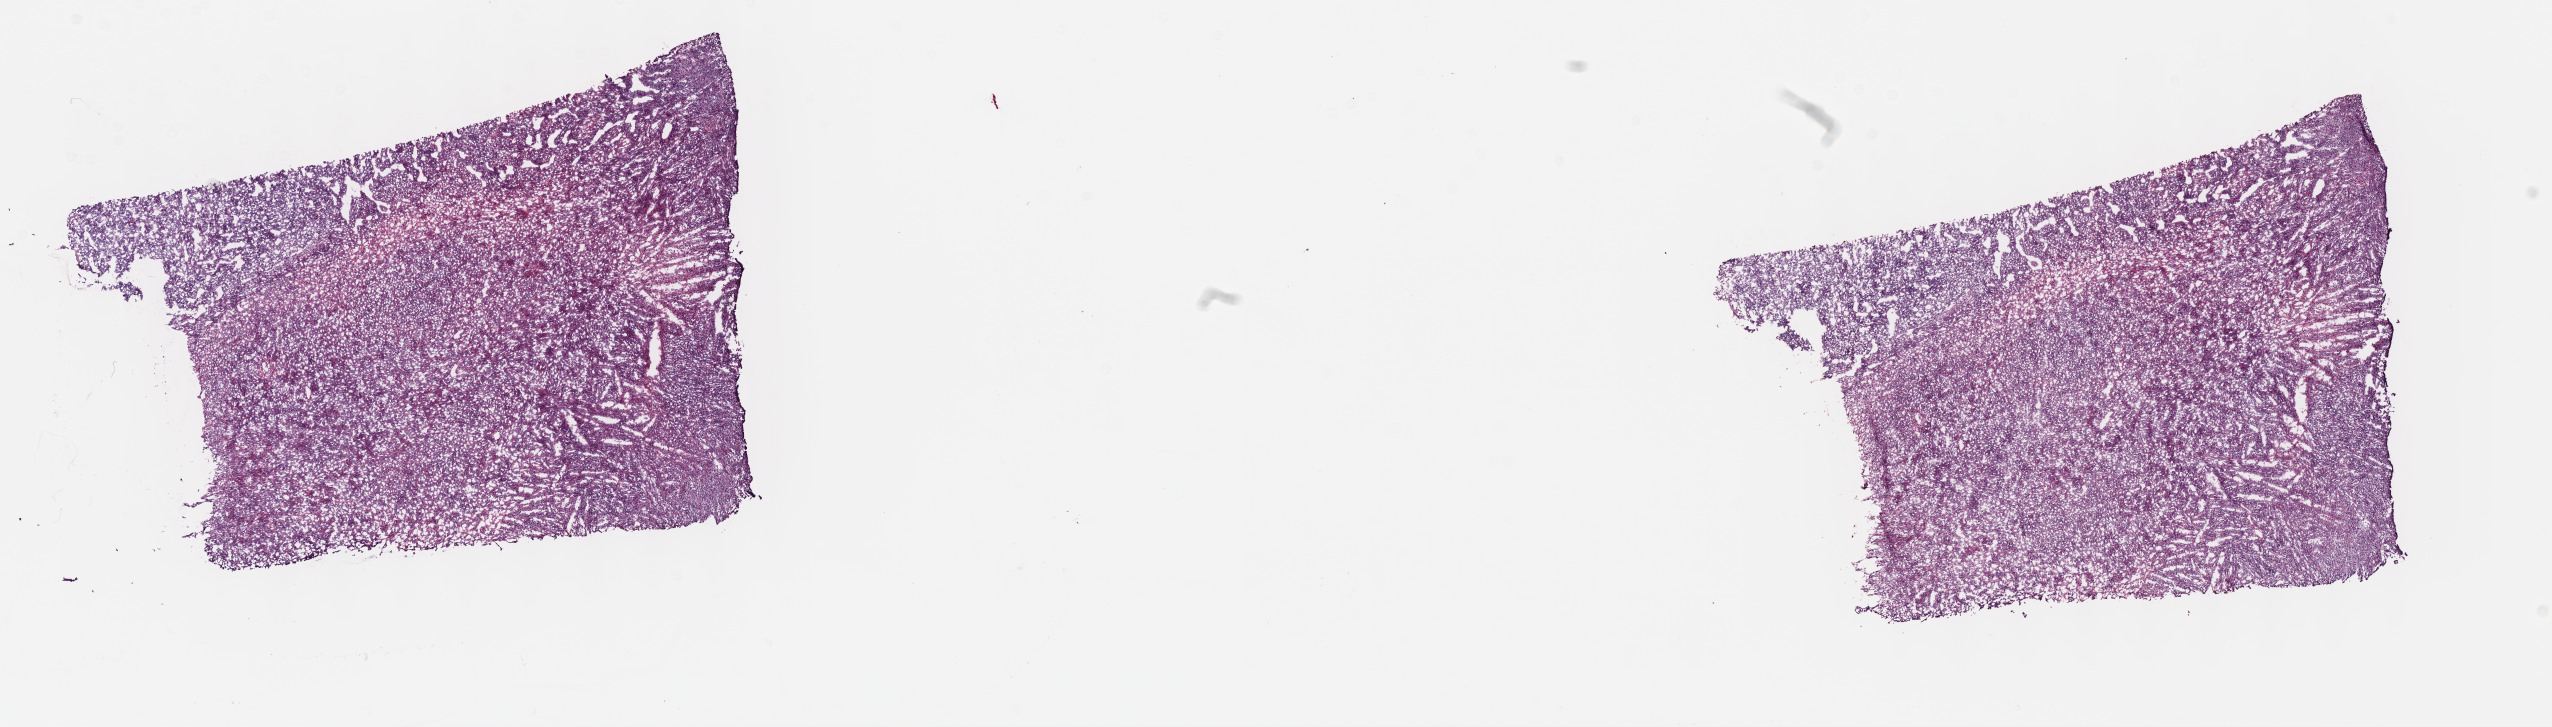
Digitized H&E tissue section (whole slide), whole scanned area (about 20.6 x 5.9 mm) shown as a low-resolution overview; frozen section from the top of the tissue portion; connective, subcutaneous and other soft tissues, primary tumour sample. Male patient; age at initial diagnosis 72 years. Pathologist review of this section (percent, as recorded): tumour cells 100%, tumour nuclei 80%.
Pathologic diagnosis: Synovial sarcoma, spindle cell (connective, subcutaneous and other soft tissues of lower limb and hip).